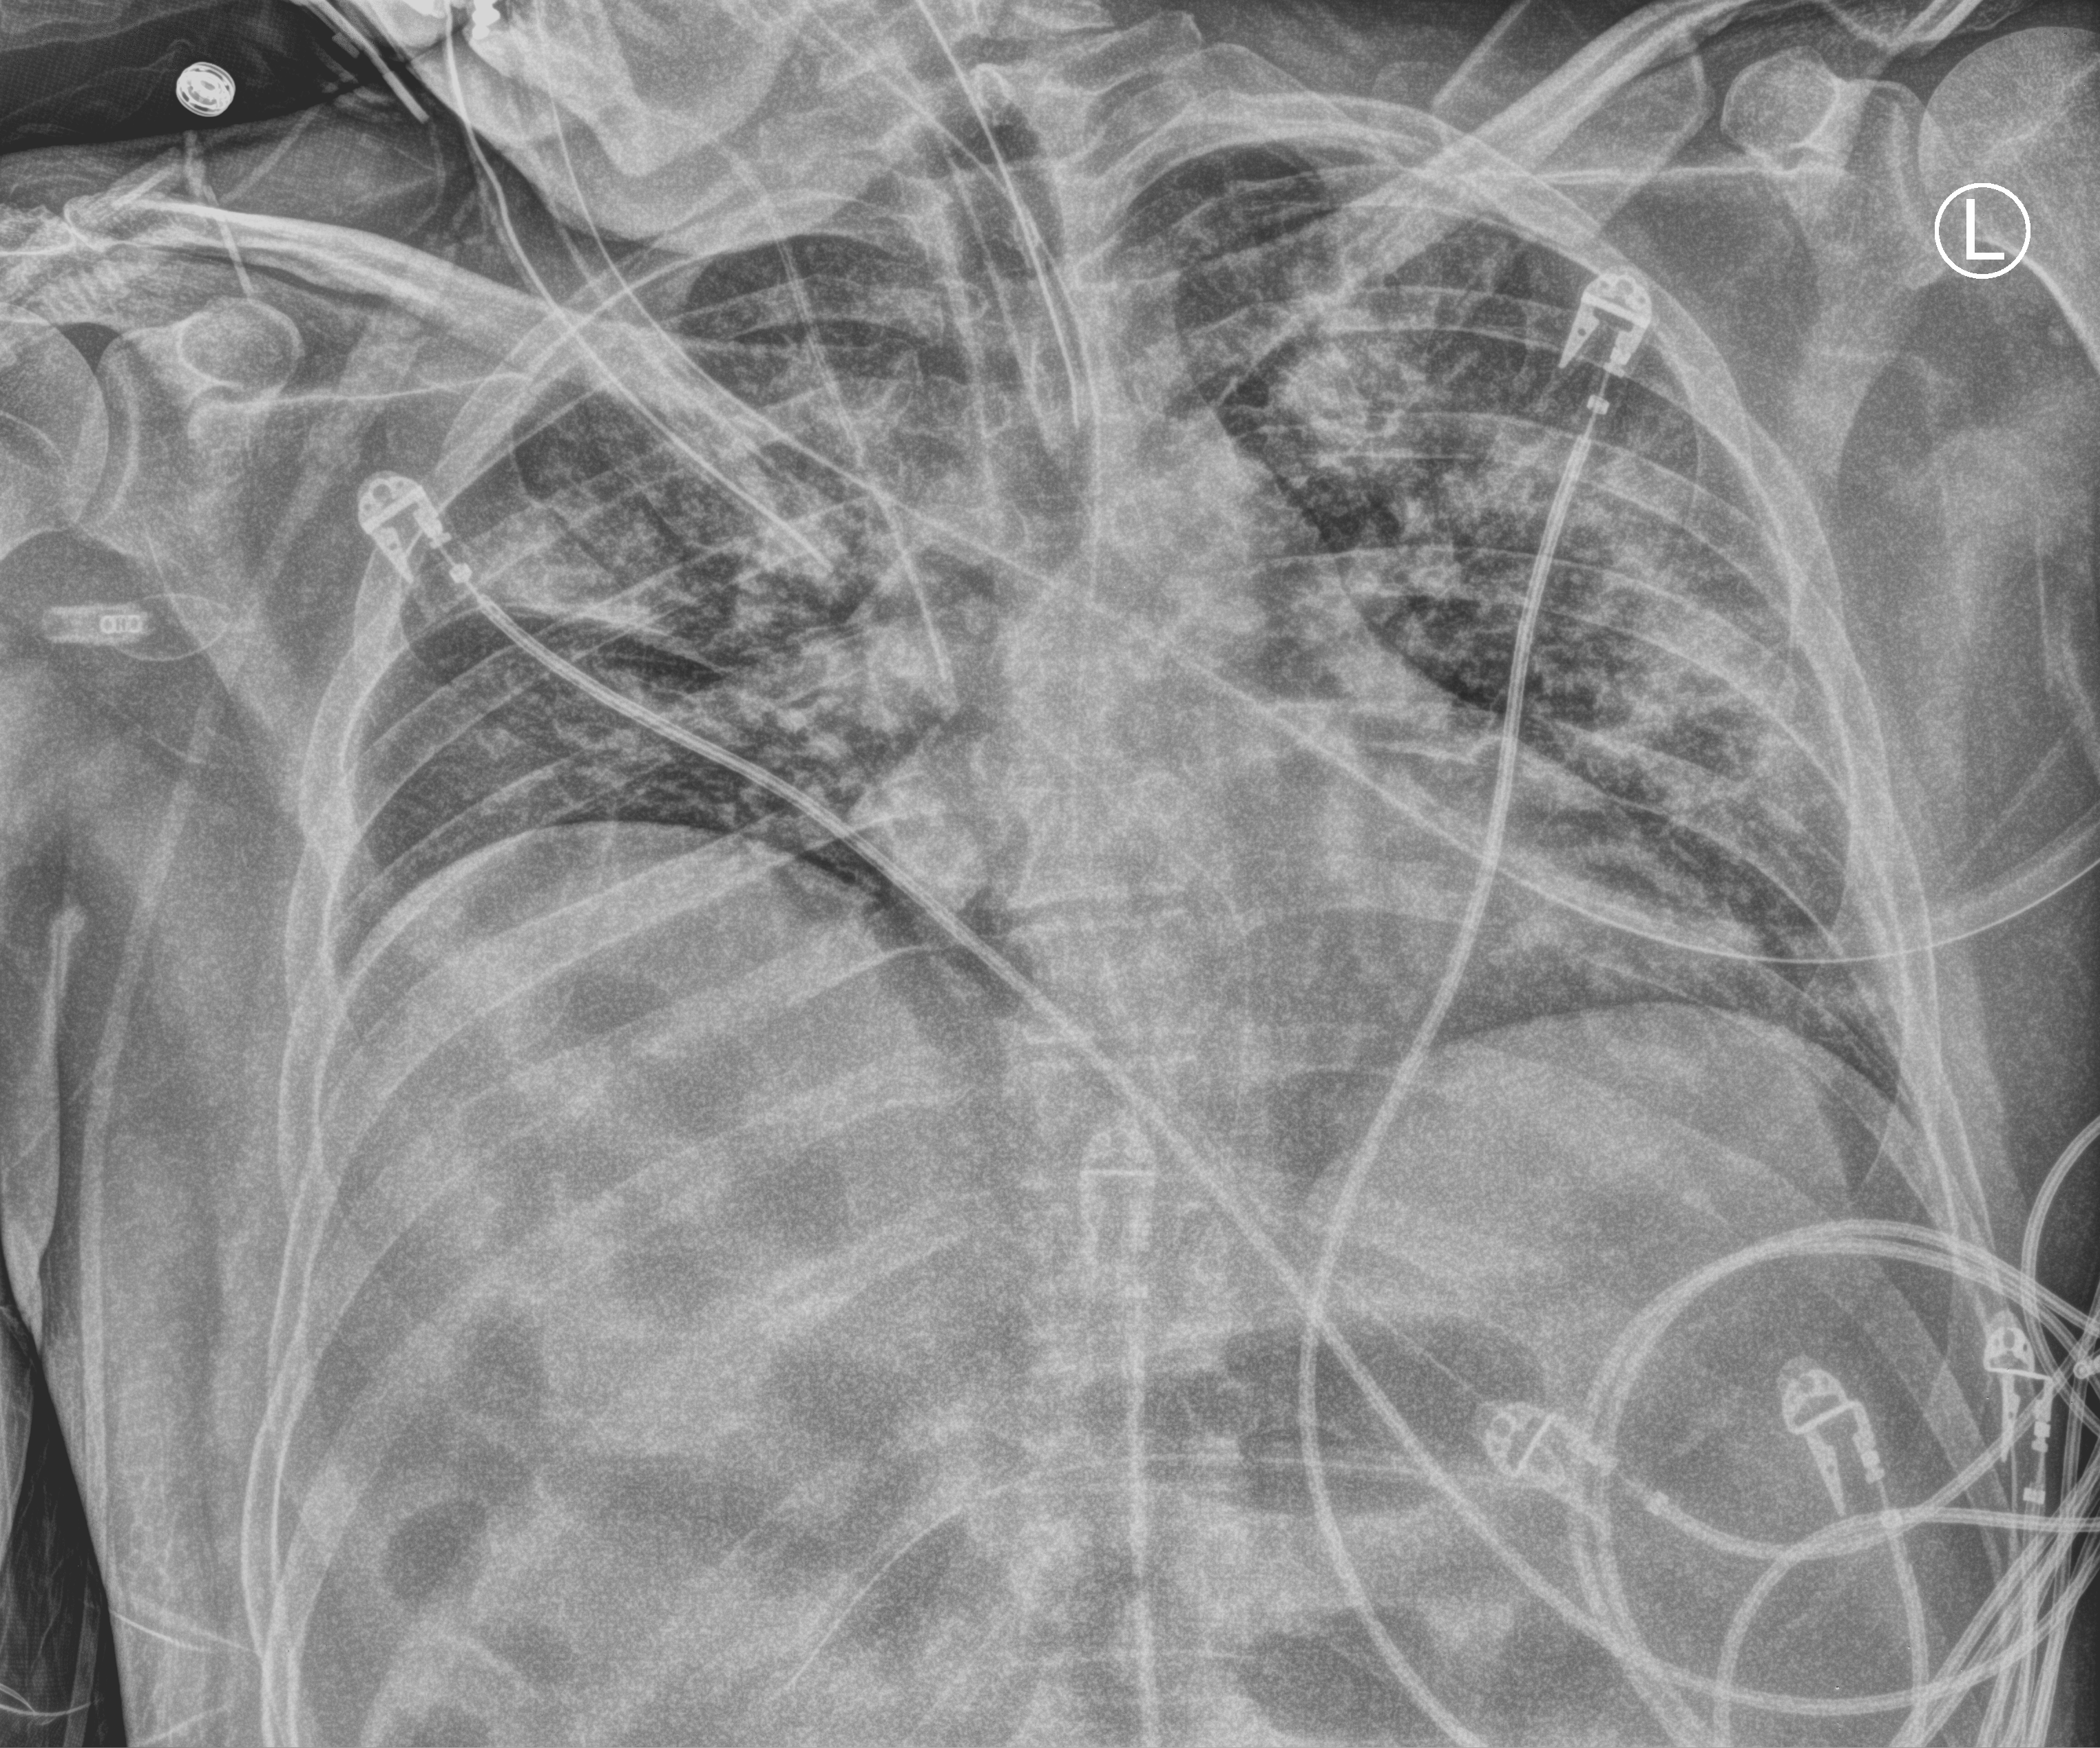
Portable chest radiograph; anteroposterior (AP) projection. Patient hospitalised with COVID-19; male, aged 18–59 years.
Hospital-stay facts (about this admission, not read from this image; timing relative to this image not recorded): mechanically ventilated during this hospital stay: yes; admitted to intensive care during this hospital stay: yes; hypertension (admission record): no.